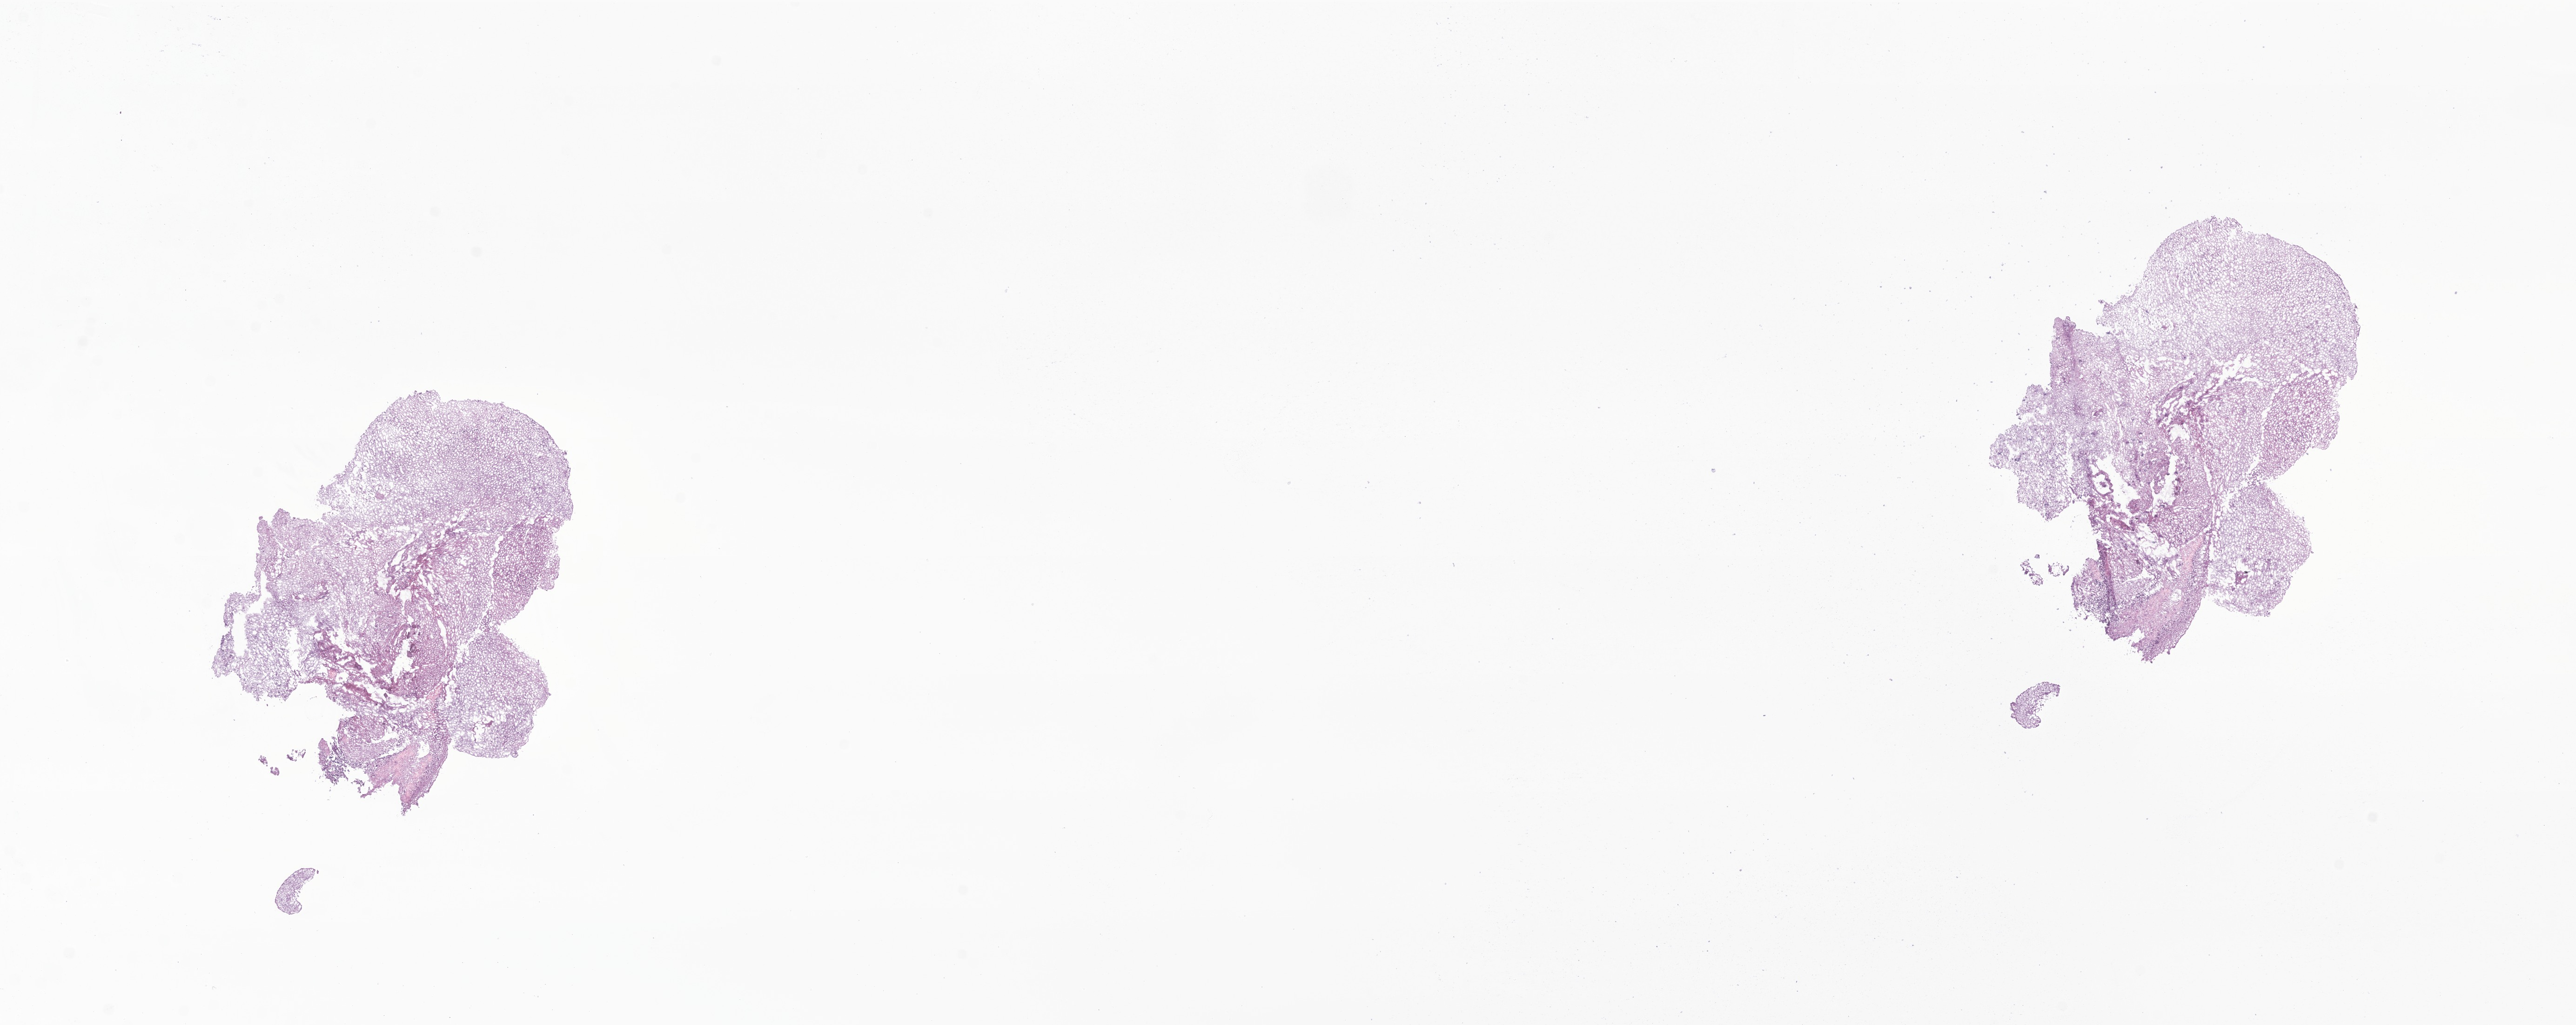
Haematoxylin and eosin whole-slide image of tumor tissue from the brain, low-resolution overview of the scanned area, about 23.3 x 9.3 mm; cryosection (OCT / tissue freezing medium). Patient male; age 178 months (14 years 10 months).
Diagnosis (ICD-O-3 morphology term): Pilocytic astrocytoma.